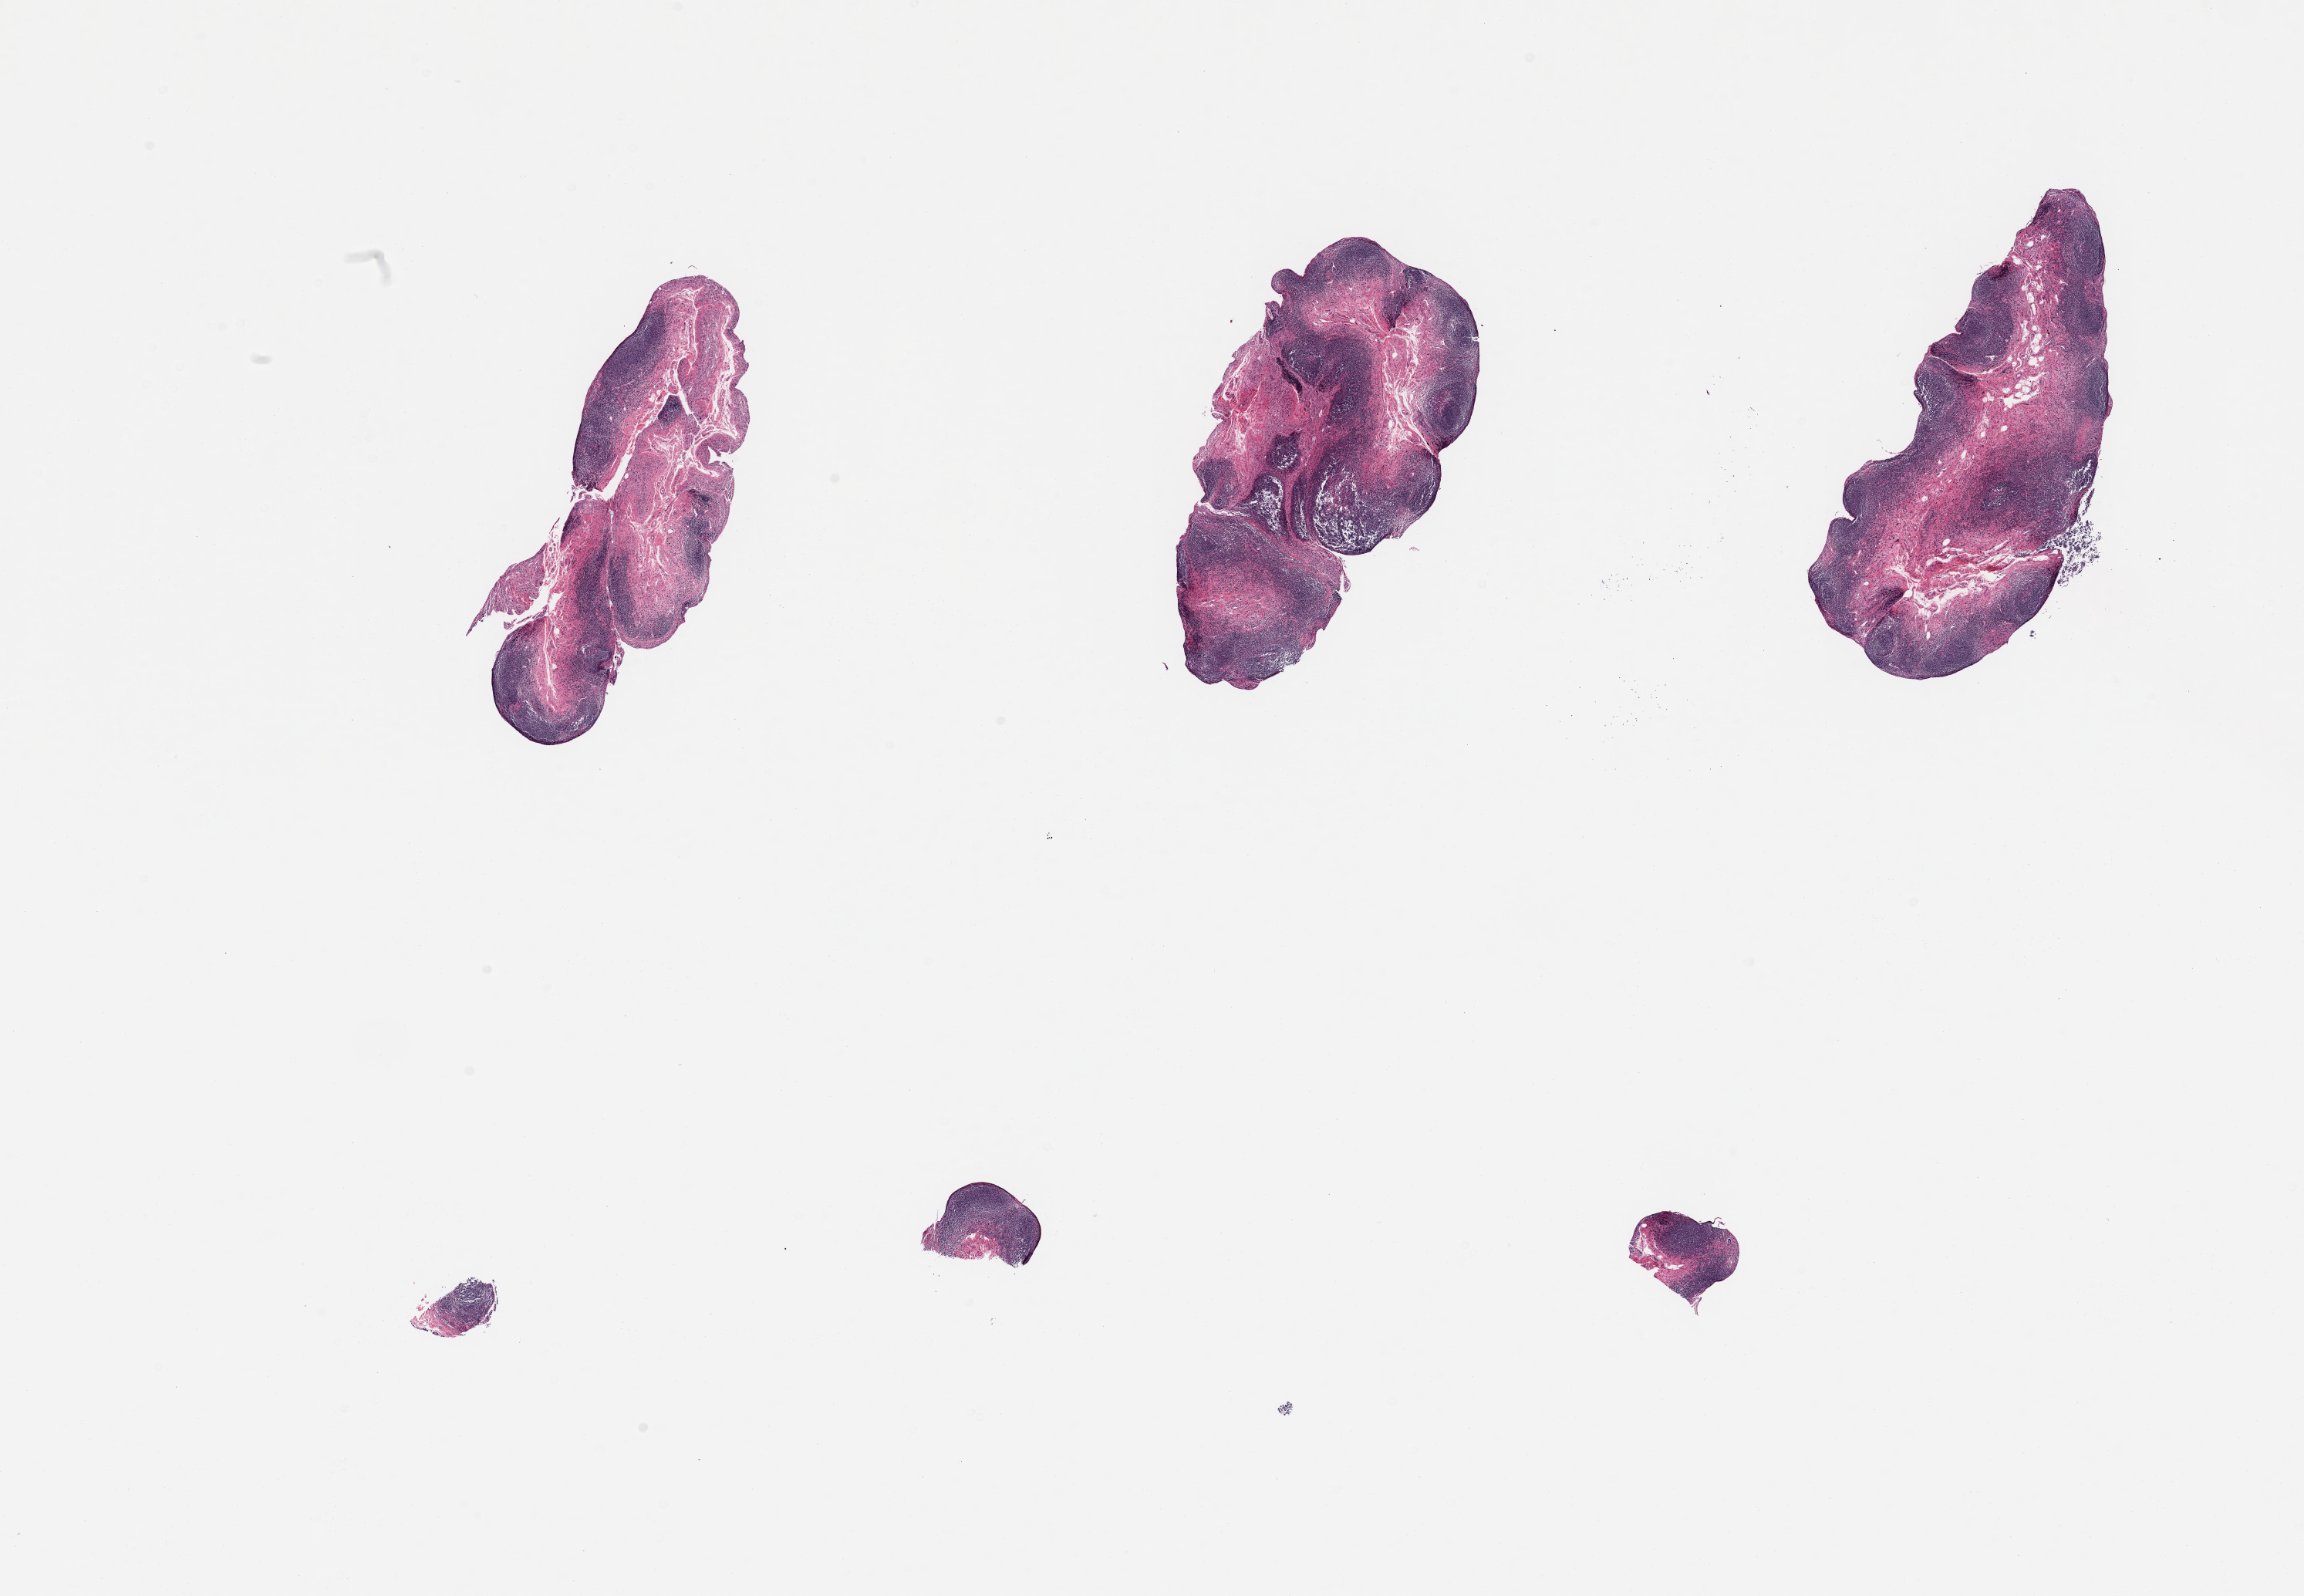
Hematoxylin and eosin (H&E) whole-slide image, whole scanned area (about 23.6 x 16.4 mm, acquisition: 20x scan) shown as a low-resolution overview. PAXgene-fixed paraffin-embedded (PFPE) section. Sampled site (target tissue): ileum. Donor tissue sample. Donor: female.
Review note (as recorded): 6 pieces, target lymphoid aggregates up to ~40% of specimen.